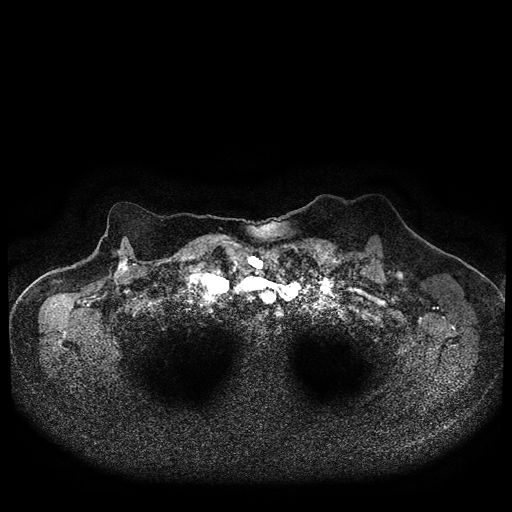
Breast MRI (dynamic contrast-enhanced, multi-phase), one axial slice. Dynamic contrast-enhanced series, time point 2 of 5 at this slice position (early post-contrast). 1.5 T. TE 2.7 ms, TR 5.4 ms. 2 mm slice thickness. 512 × 512 image matrix, field of view 340 × 340 mm. Female patient, age 72 years.
Annotated regions visible in this slice (semi-automatic segmentation, software-assisted and operator-edited):
- breast lesion (labelled 'tumour' in the annotation; benign lesions carry a separate 'benign' label): bounding box <117,254,130,275> (left, top, right, bottom; pixels)